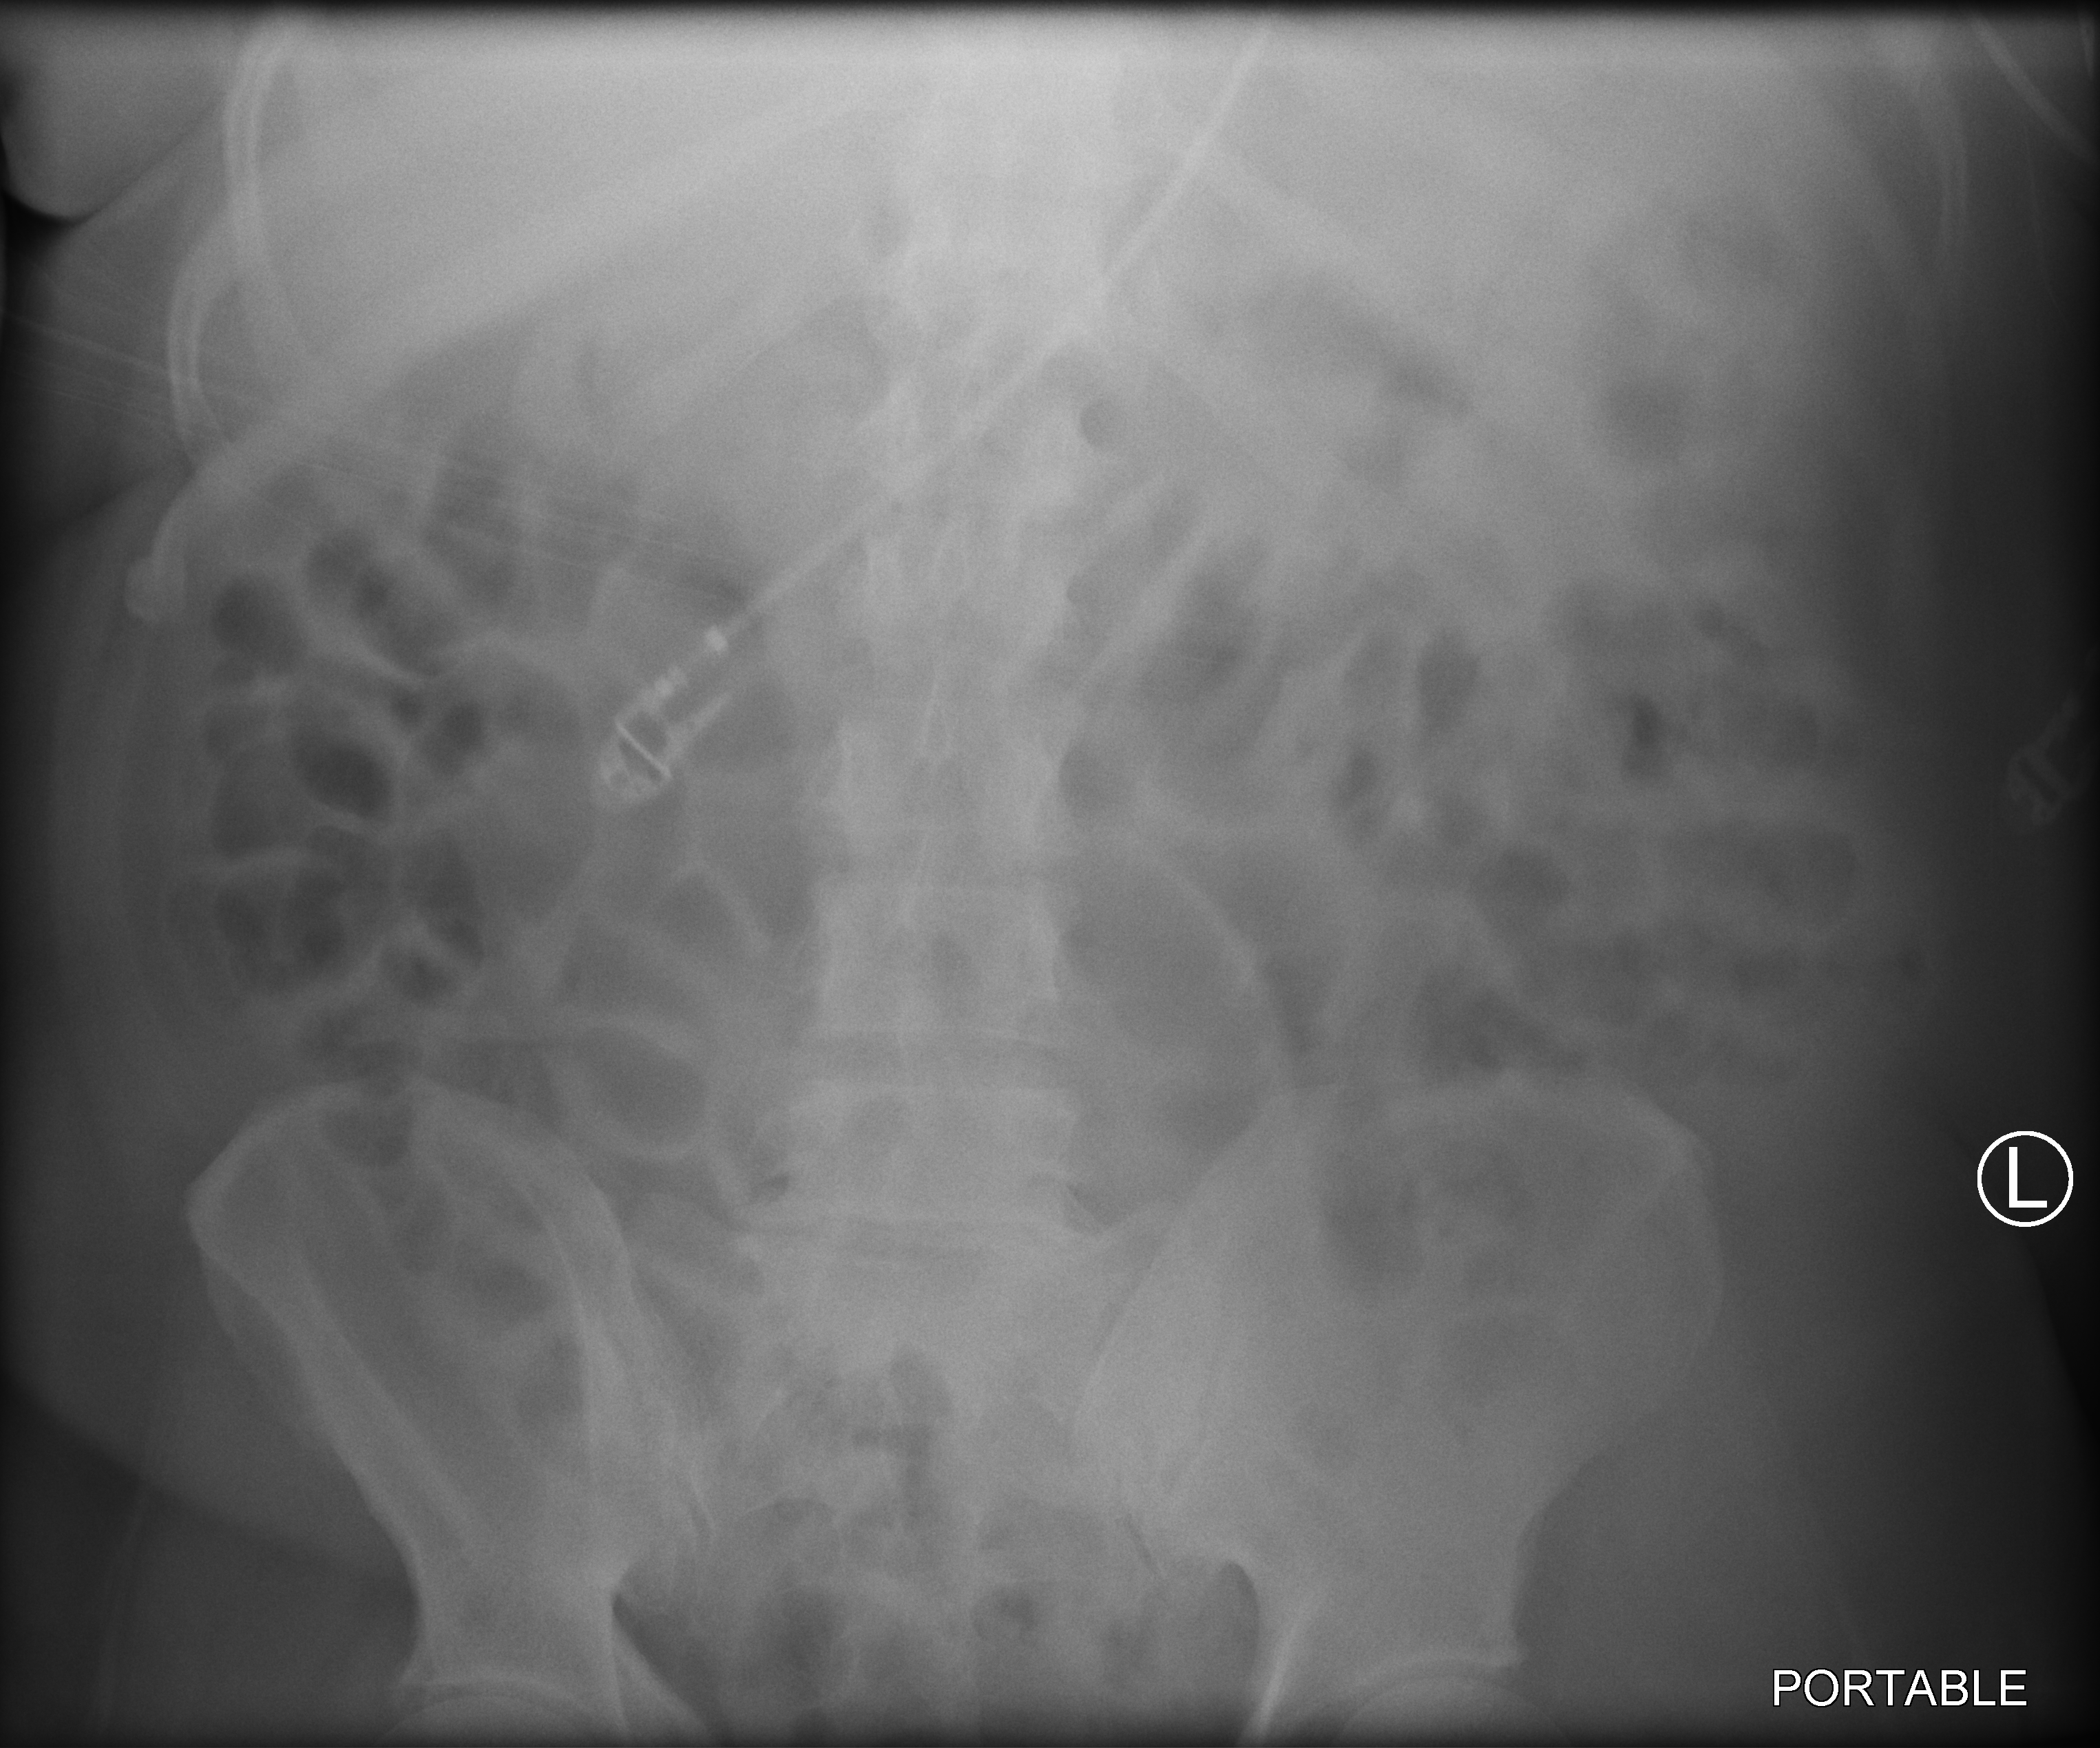
Abdomen radiograph (computed radiography), anteroposterior (AP) projection. Patient hospitalised with COVID-19; male, aged 60–74 years.
Admission-level facts for this patient (not findings on this image; timing relative to this image not recorded): mechanically ventilated during this hospital stay: yes; admitted to intensive care during this hospital stay: yes.